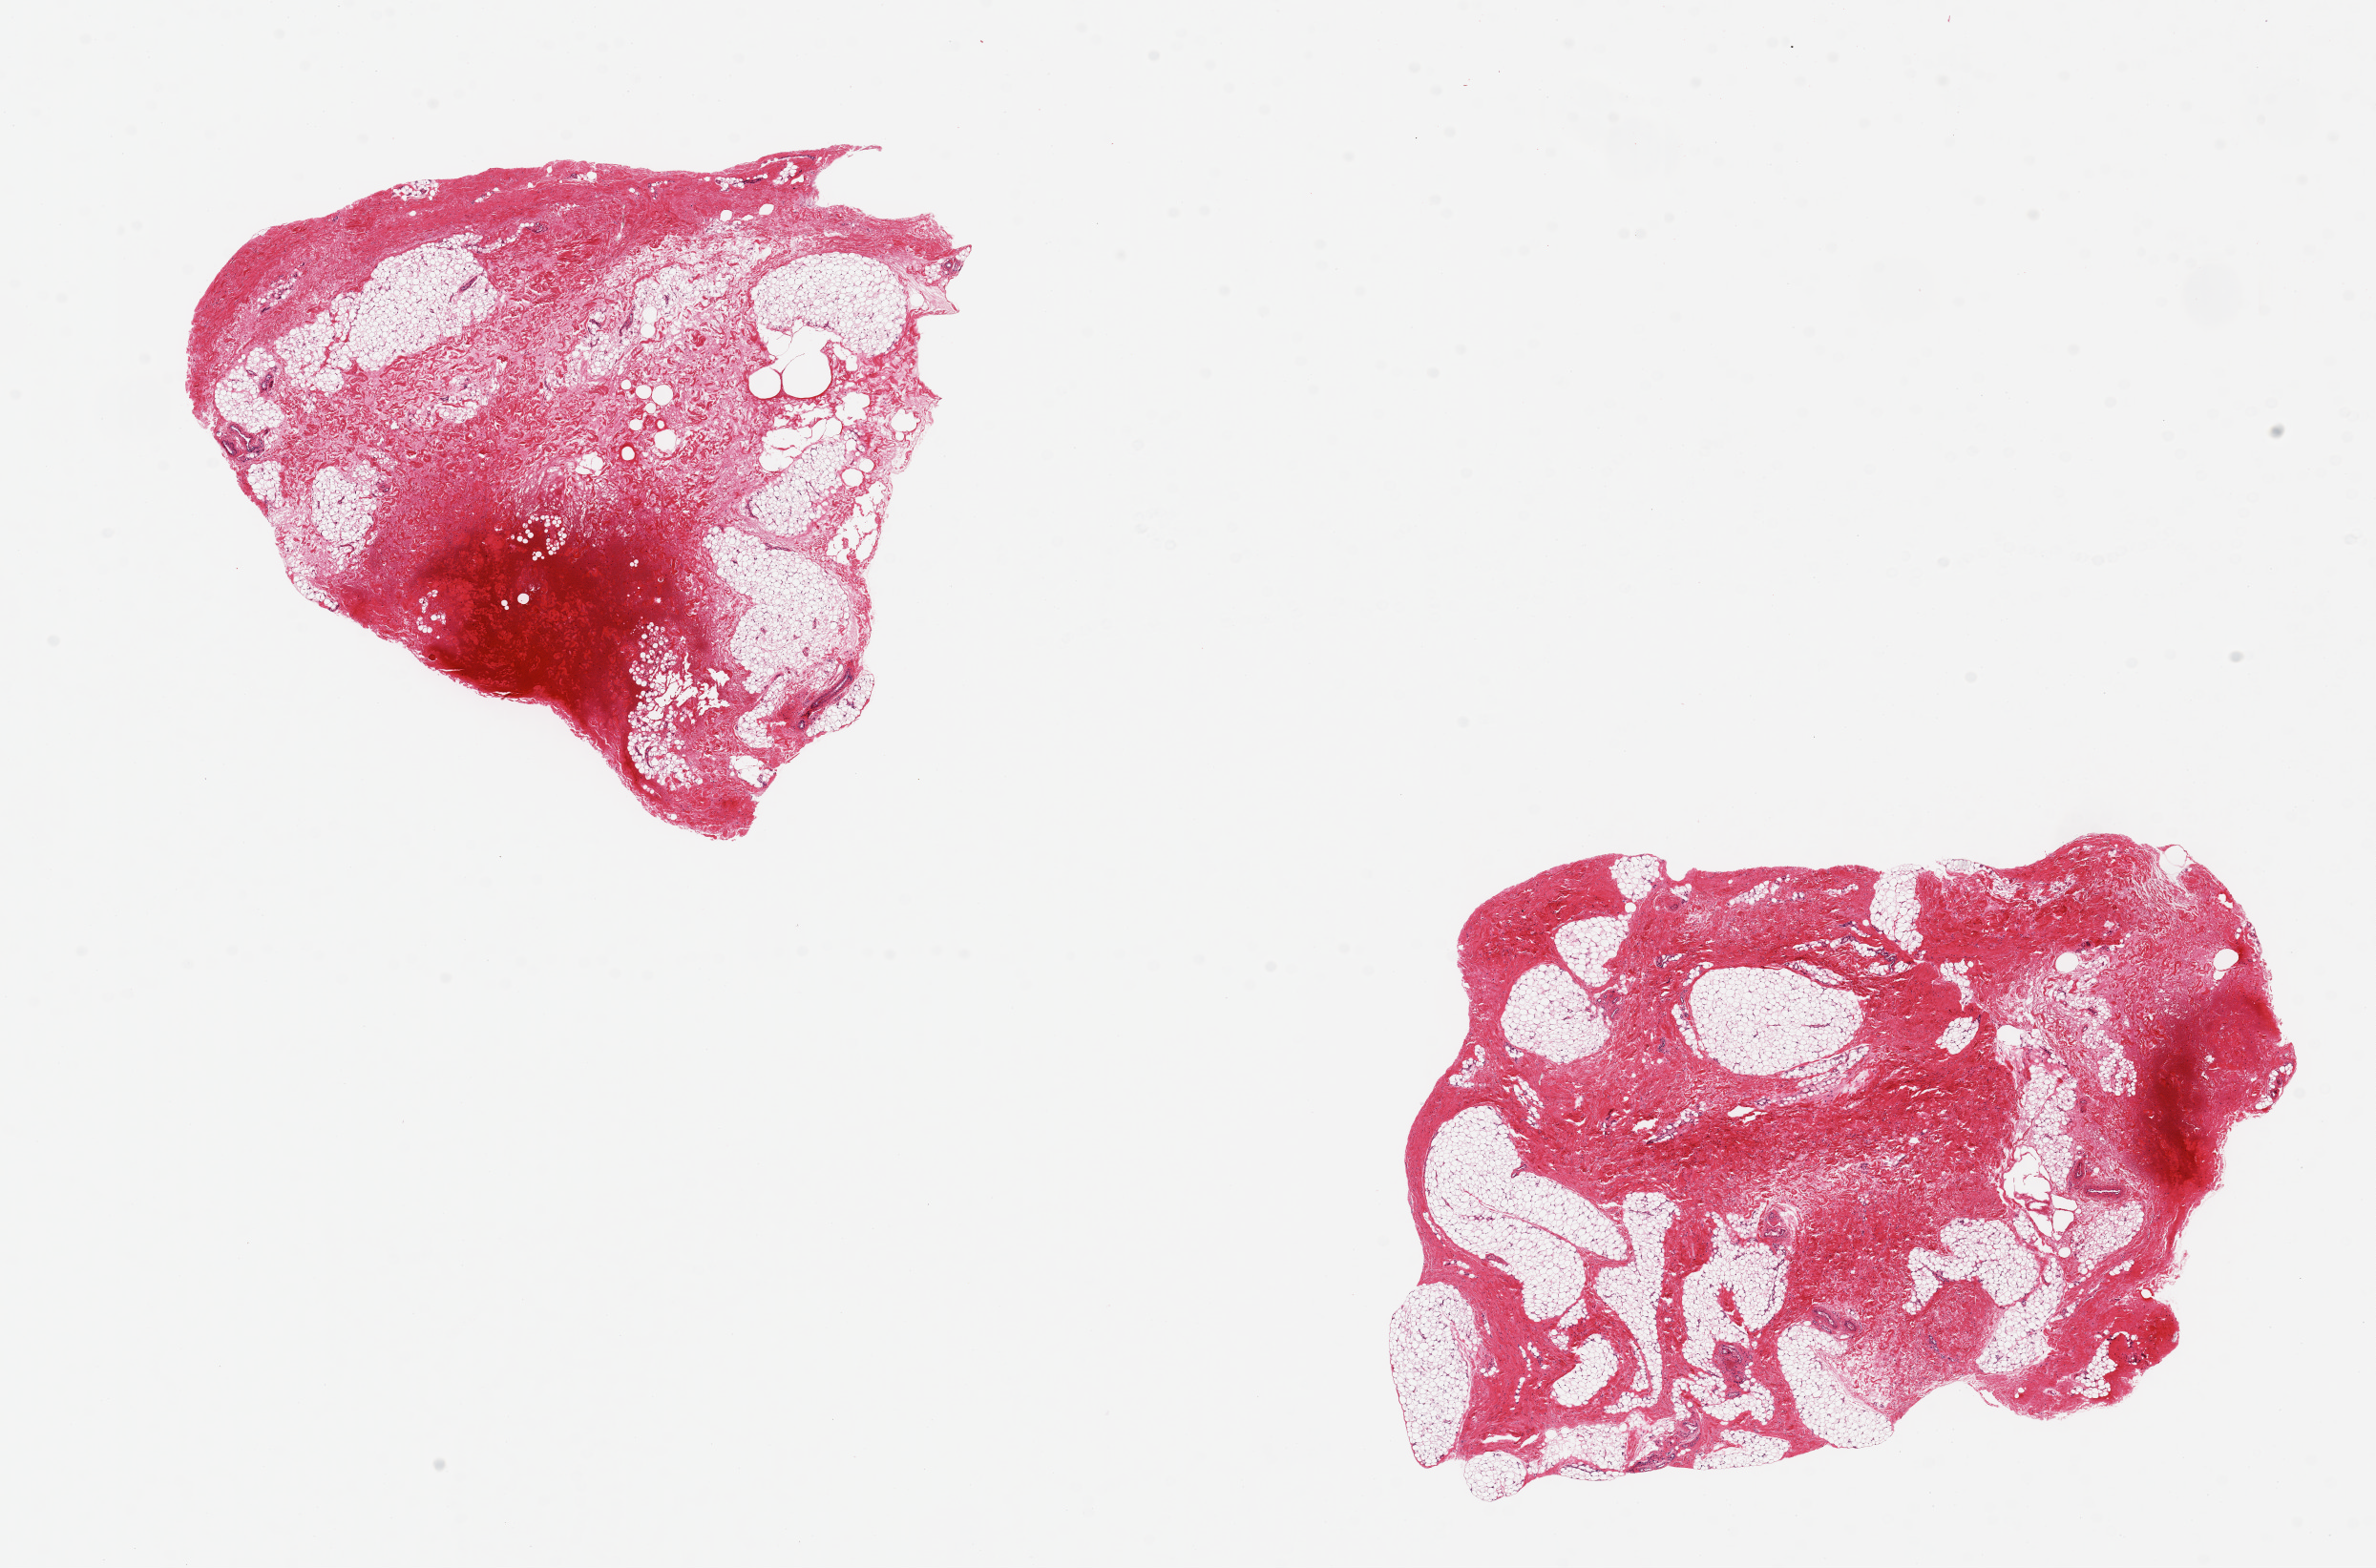
Whole-slide image, haematoxylin and eosin stain, brightfield, whole scanned area (about 19.7 x 13.0 mm) shown as a low-resolution overview, PAXgene-fixed paraffin-embedded (PFPE) section, section of breast (target tissue), tissue donor sample. Donor: male.
- review note (as recorded): 2 pieces ~6x5mm. No ductal elements, both hemorrhagic probably secondary to trauma (by history)